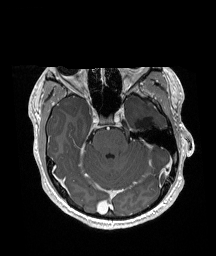
Brain MRI from a brain-tumour surgery series, one axial slice; slice 121 of 192 in the series (ordered by position); T1-weighted post-contrast; 1 mm slice thickness; 216 × 256 image matrix, field of view 211 × 250 mm. From the clinical record (not read from this slice): histopathology: Glioneuronal tumor; WHO grade: 2.
Structures marked on this image (outlined manually by an expert reader):
- previous resection cavity: bounding box (x1, y1, x2, y2) in pixels: (136, 116, 154, 133)